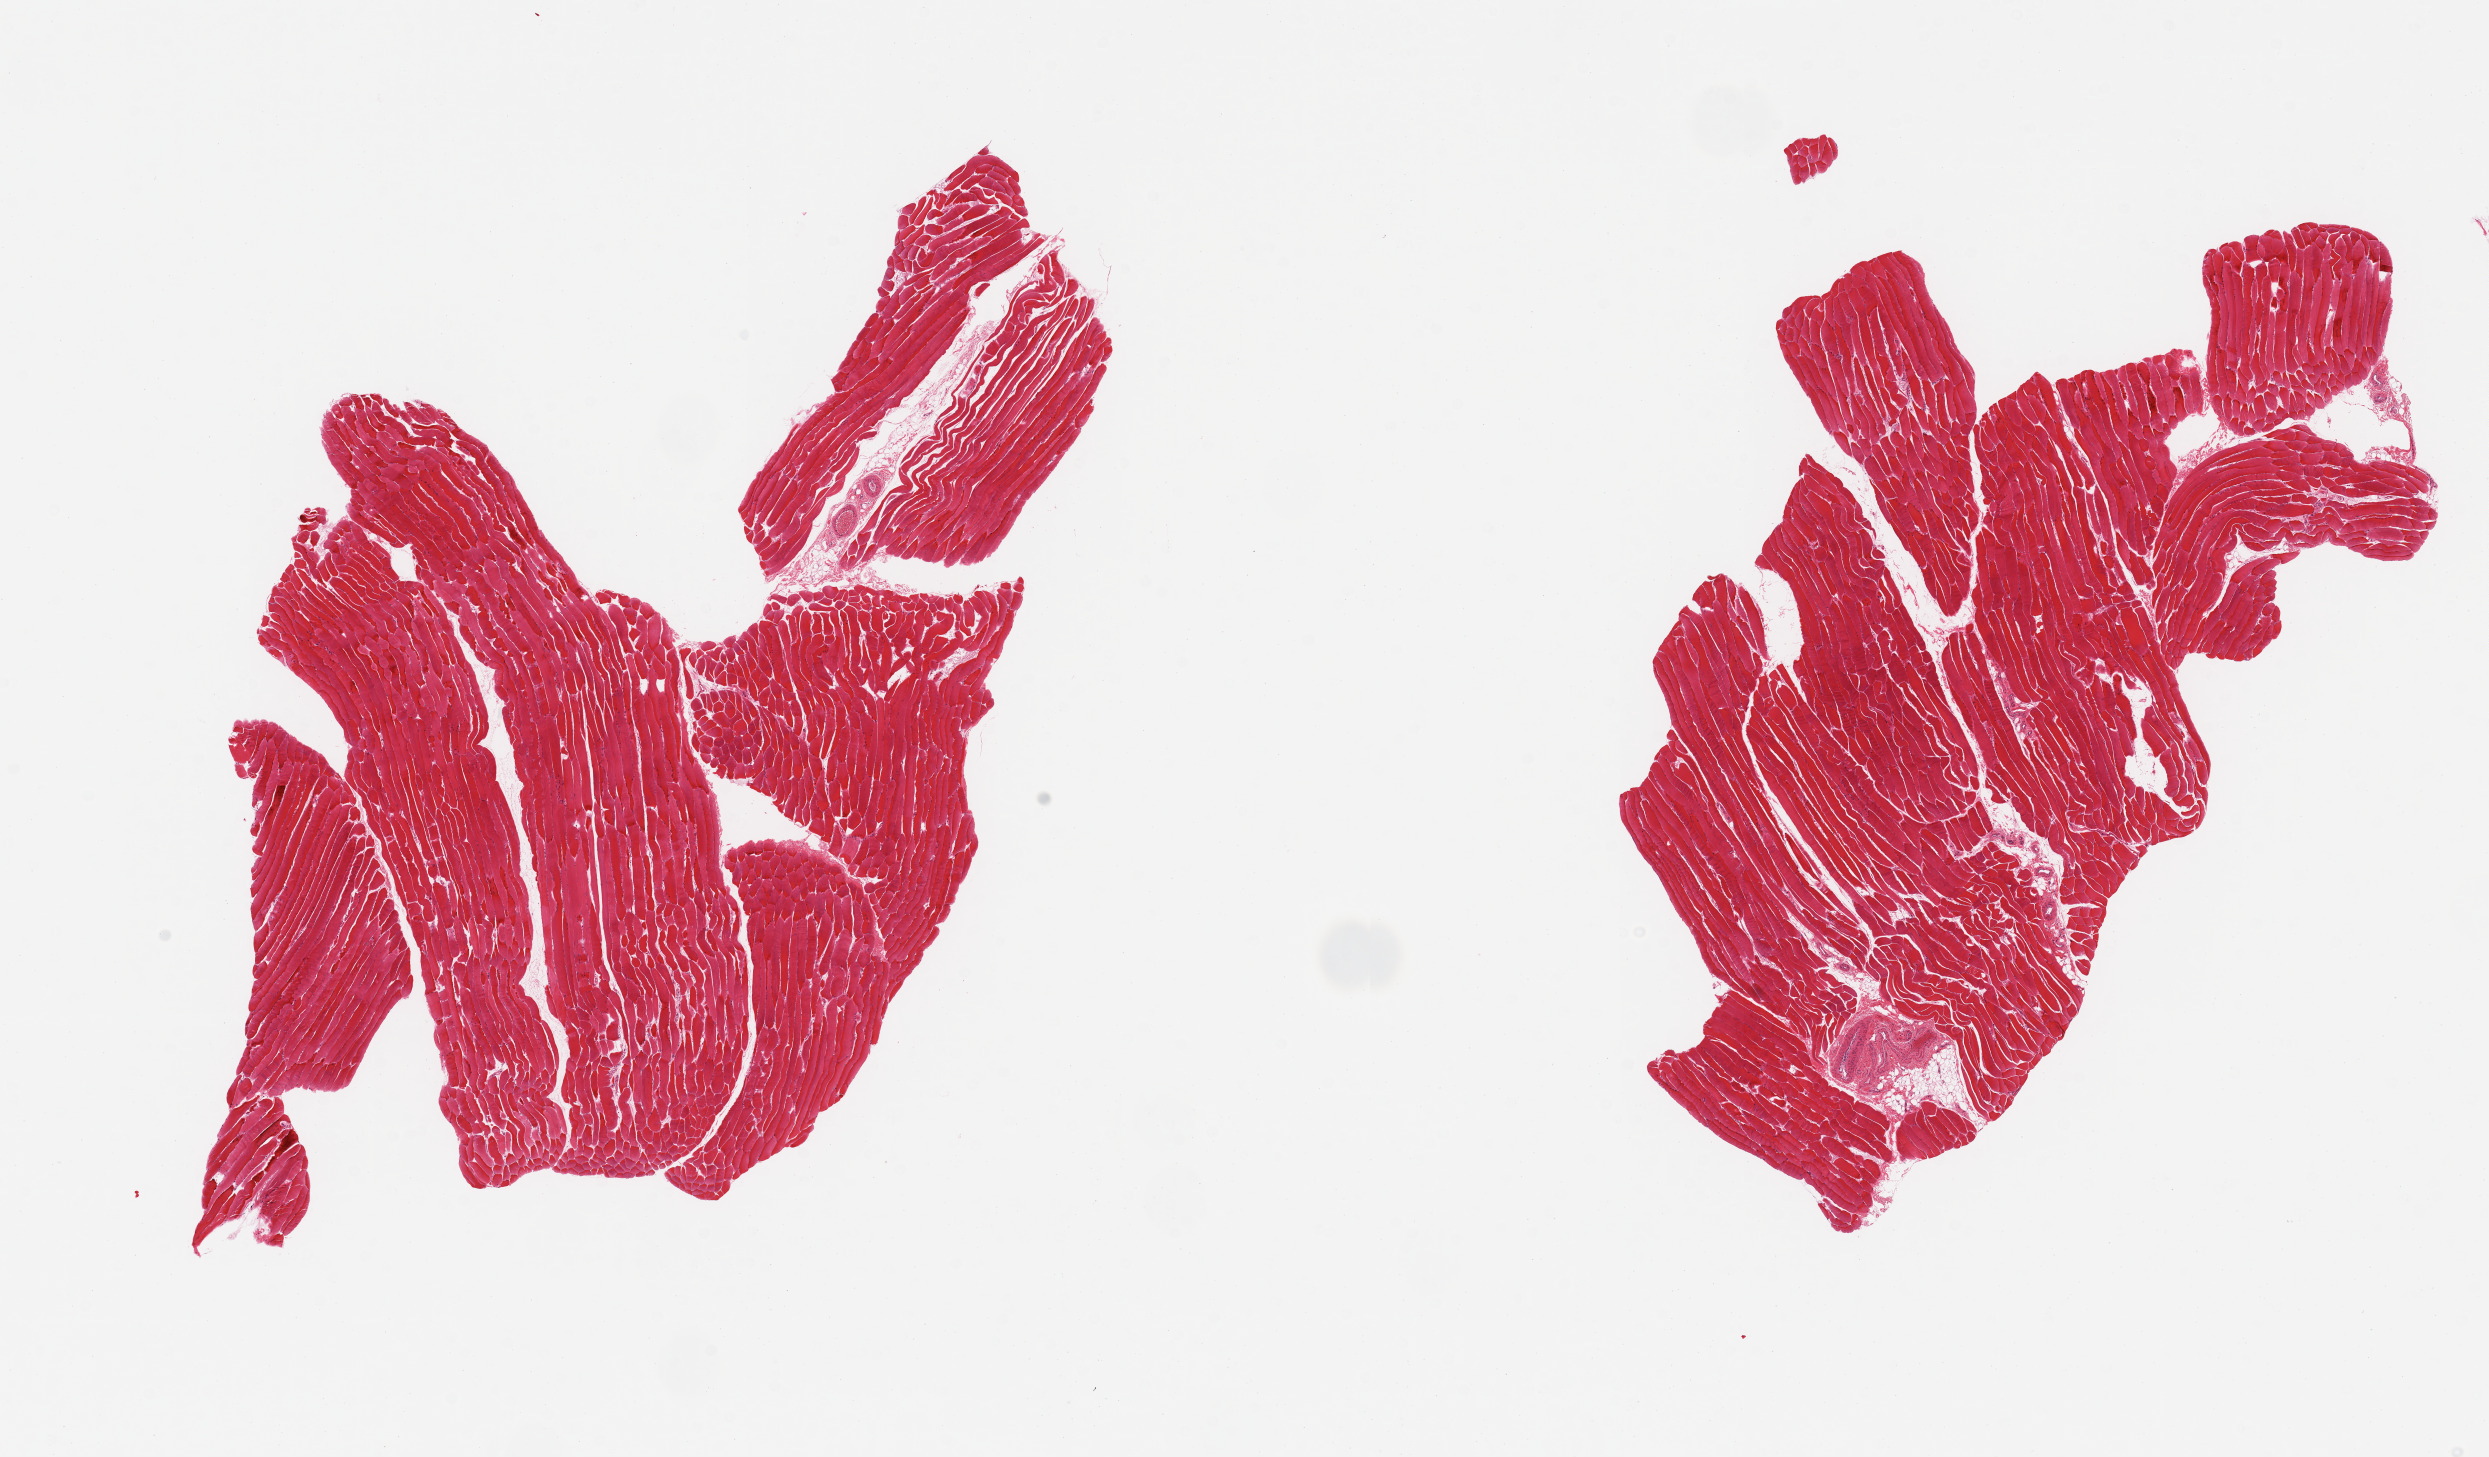
Digitized H&E-stained section — whole scanned area (about 19.7 x 11.5 mm) shown as a low-resolution overview, PAXgene-fixed, paraffin-embedded tissue, sampled site (target tissue): skeletal muscle, donor tissue sample. Male donor.
* review note (as recorded): 2 pieces; skeletal muscle with small focus of vessels/fat